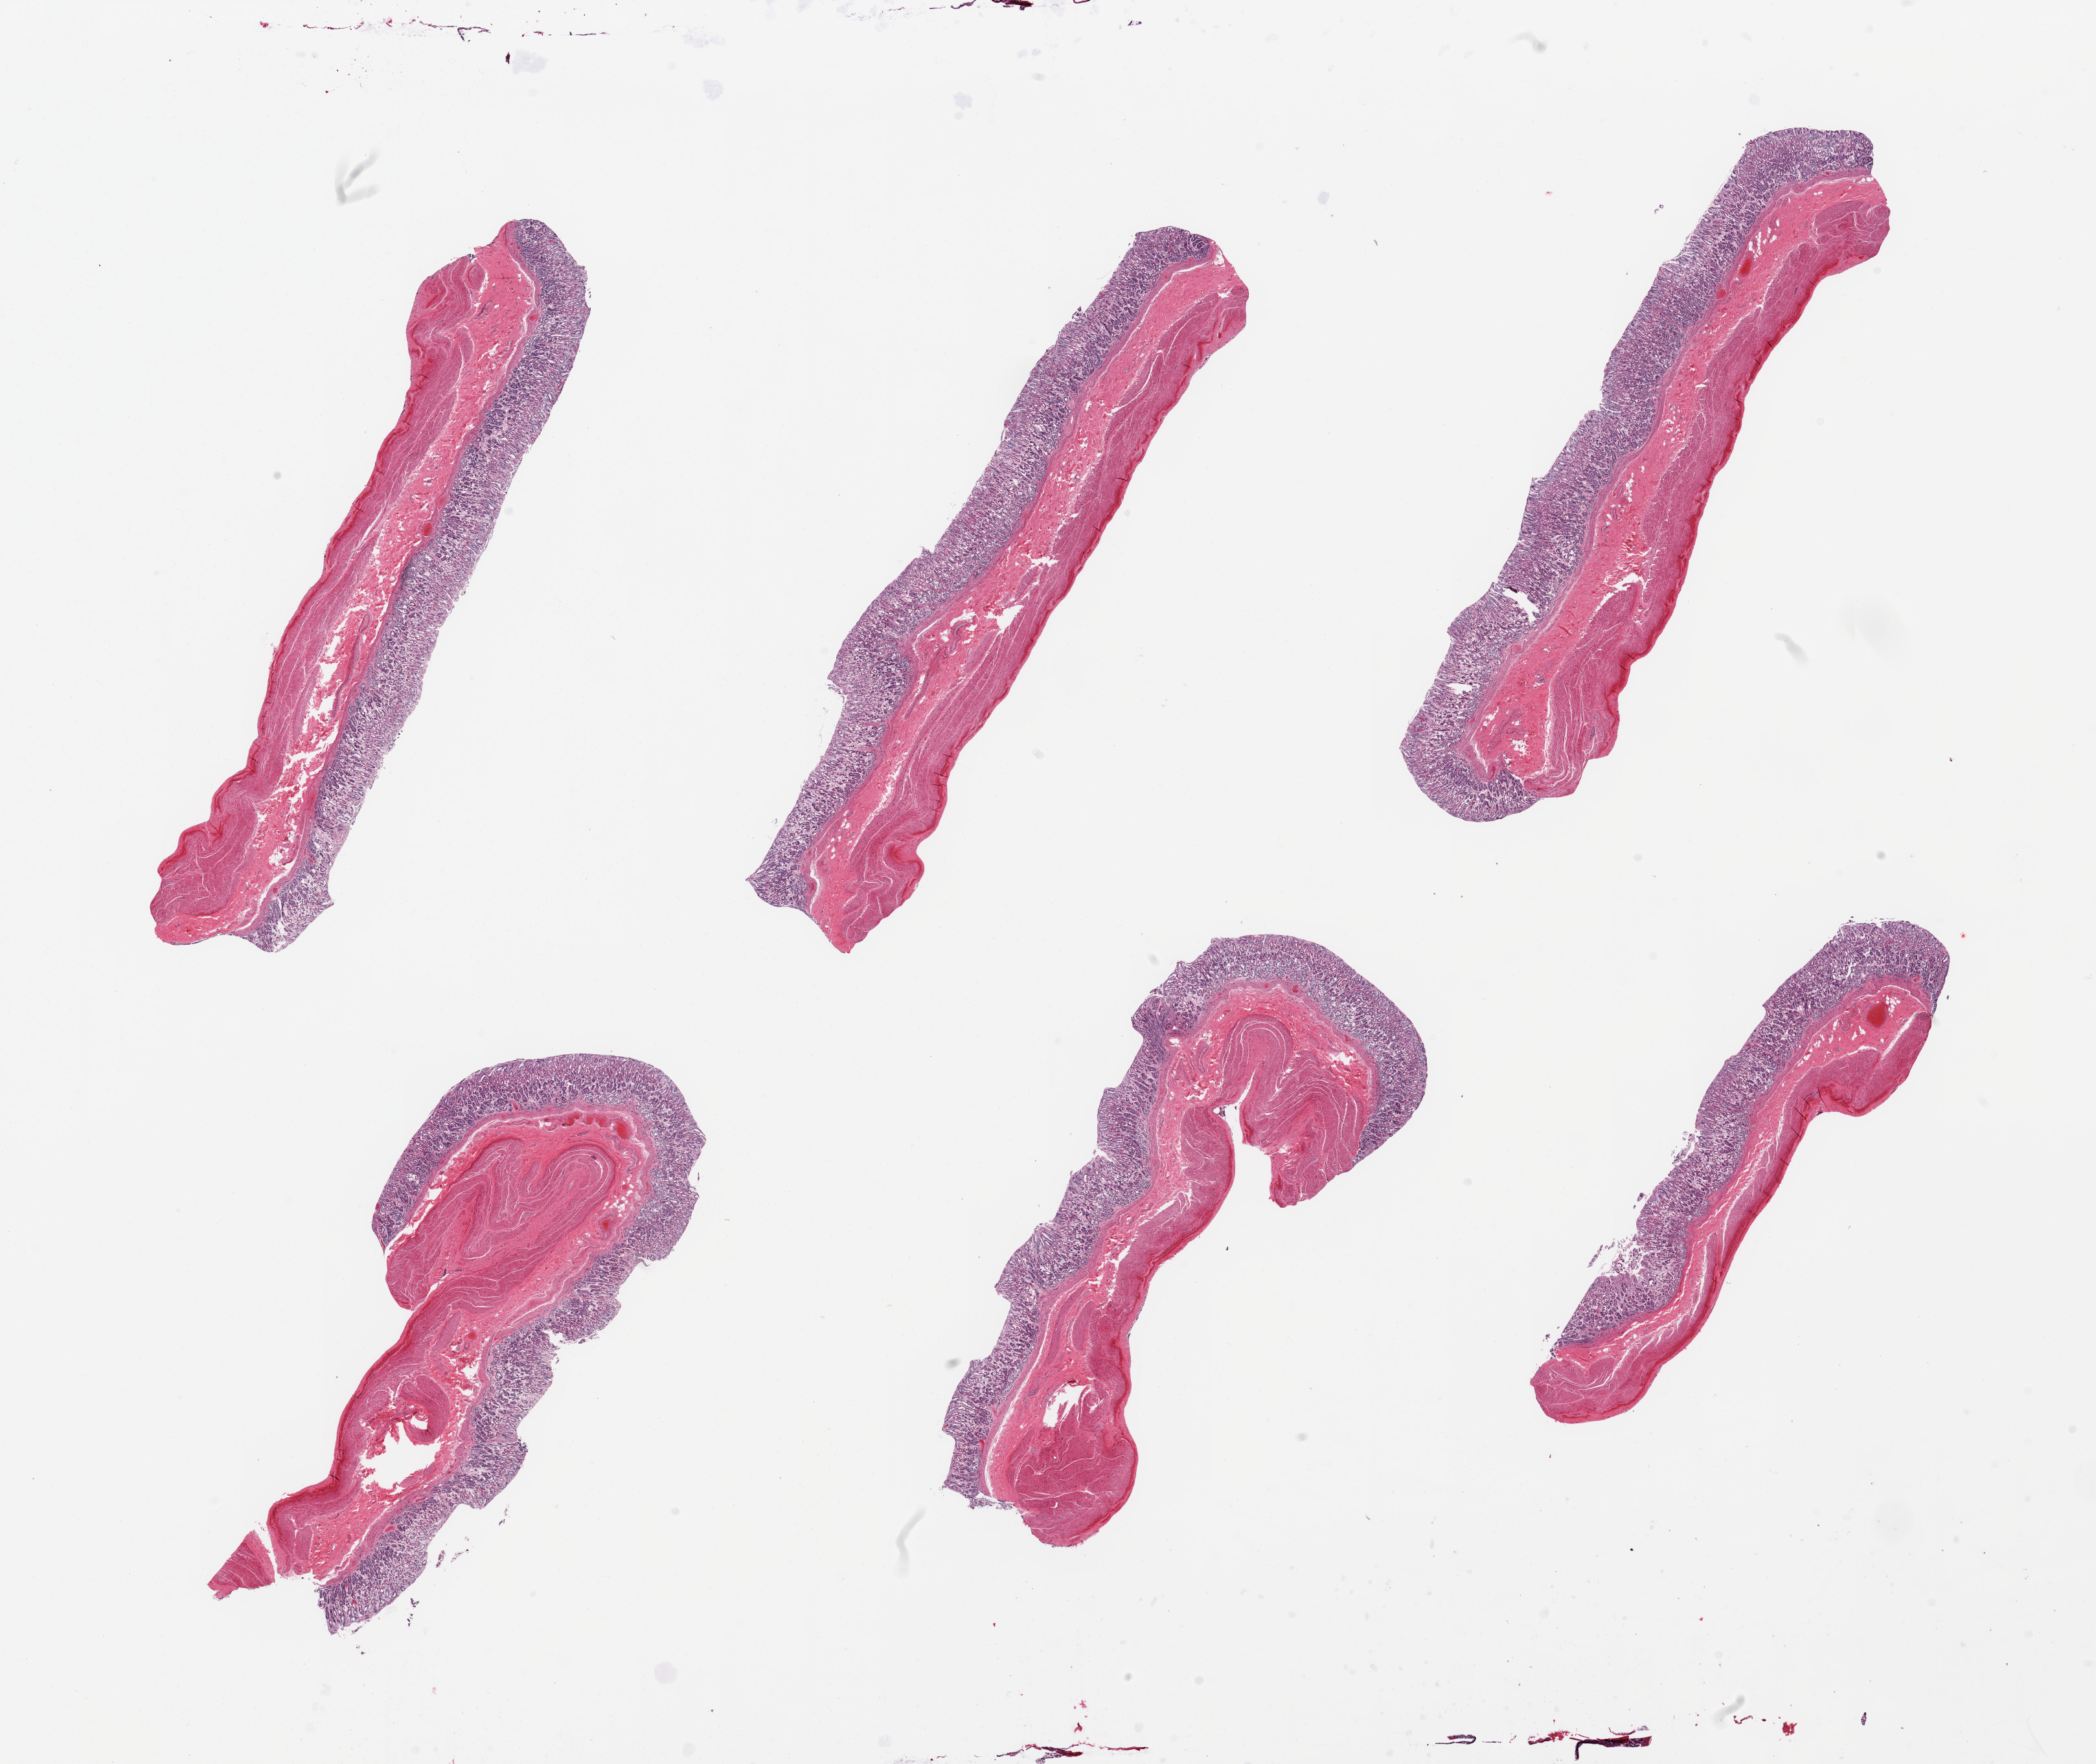
Whole-slide image, hematoxylin and eosin (H&E) stain, brightfield, whole scanned area (about 25.6 x 21.5 mm) shown as a low-resolution overview, PAXgene-fixed, paraffin-embedded tissue, sampled site (target tissue): stomach, donor tissue sample. Donor sex: male.
• reviewer comment on this tissue sample: 6 pieces; mucosa moderately autolyzed focally